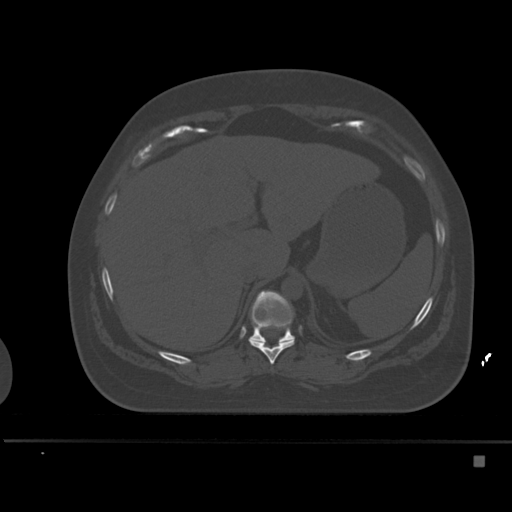
CT including the spine, one axial slice. Slice 241 of 495 in the series (ordered by position). Bone window (W 1800 / L 400 HU). 512 × 512 image matrix, field of view 404 × 404 mm. Patient: female, 33 years. From the clinical record (not read from this slice): primary cancer: breast.
Structures marked on this image (semi-automatic segmentation, software-assisted and operator-edited):
- T10 vertebra: bounding box (x1, y1, x2, y2) in pixels: (249, 324, 295, 365)
- T11 vertebra: (249, 291, 295, 343)